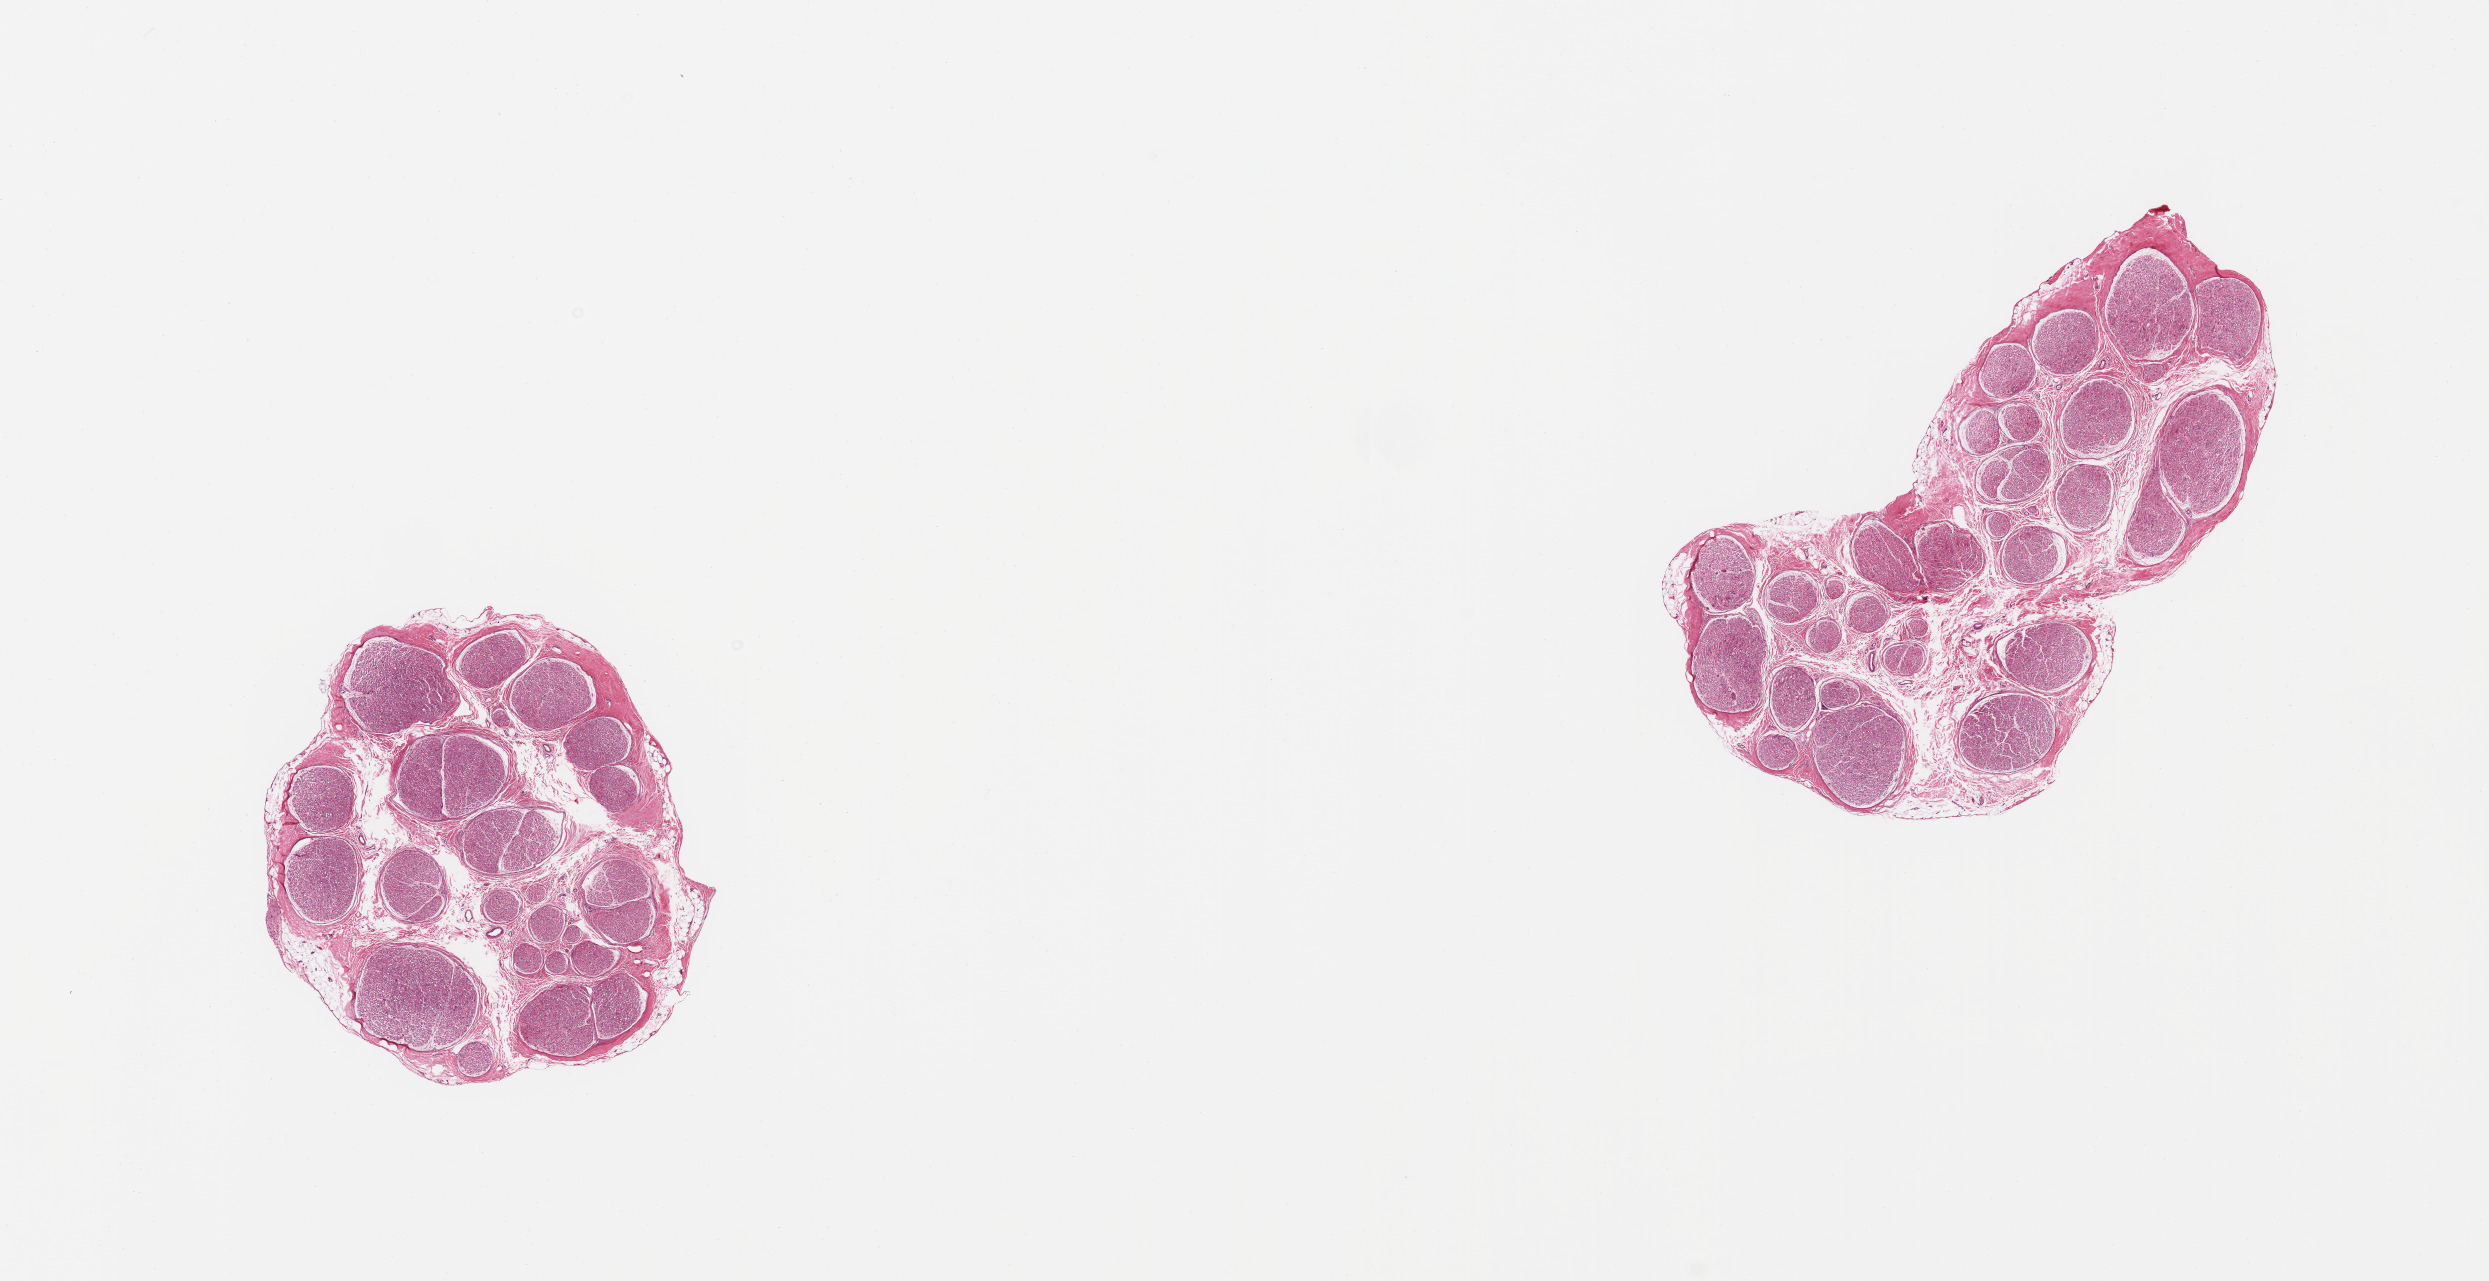
Digitized H&E-stained section, whole scanned area (about 19.7 x 10.1 mm) shown as a low-resolution overview; PAXgene-fixed paraffin-embedded (PFPE) section; section of tibial nerve (target tissue); tissue donor sample.
* reviewer comment on this tissue sample: 2 pieces, no adherent fat